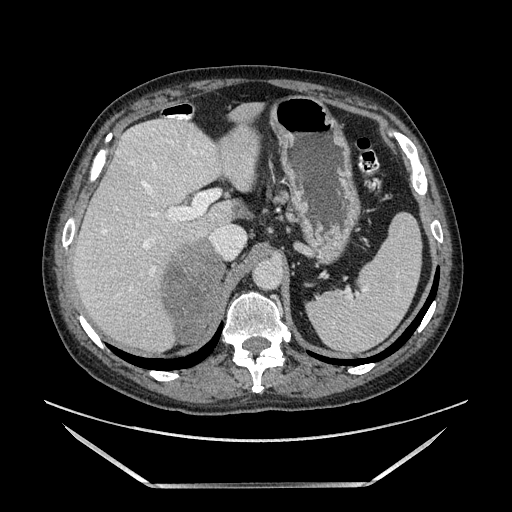
Contrast-enhanced abdominal CT, one axial slice; slice 102 of 185 in the series (ordered by position); soft-tissue window (W 400 / L 40 HU); 512 × 512 image matrix. Male patient. From the clinical record (not read from this slice): diagnosis: adrenocortical carcinoma; tumour side: right adrenal; tumour size at pathology: 10.3 cm; Ki-67 index: 20 %; stage (as recorded): 3.
Outlined on this slice (semi-automatic segmentation, software-assisted and operator-edited):
- mass: bounding box [x1, y1, x2, y2] px = [164, 236, 226, 344]